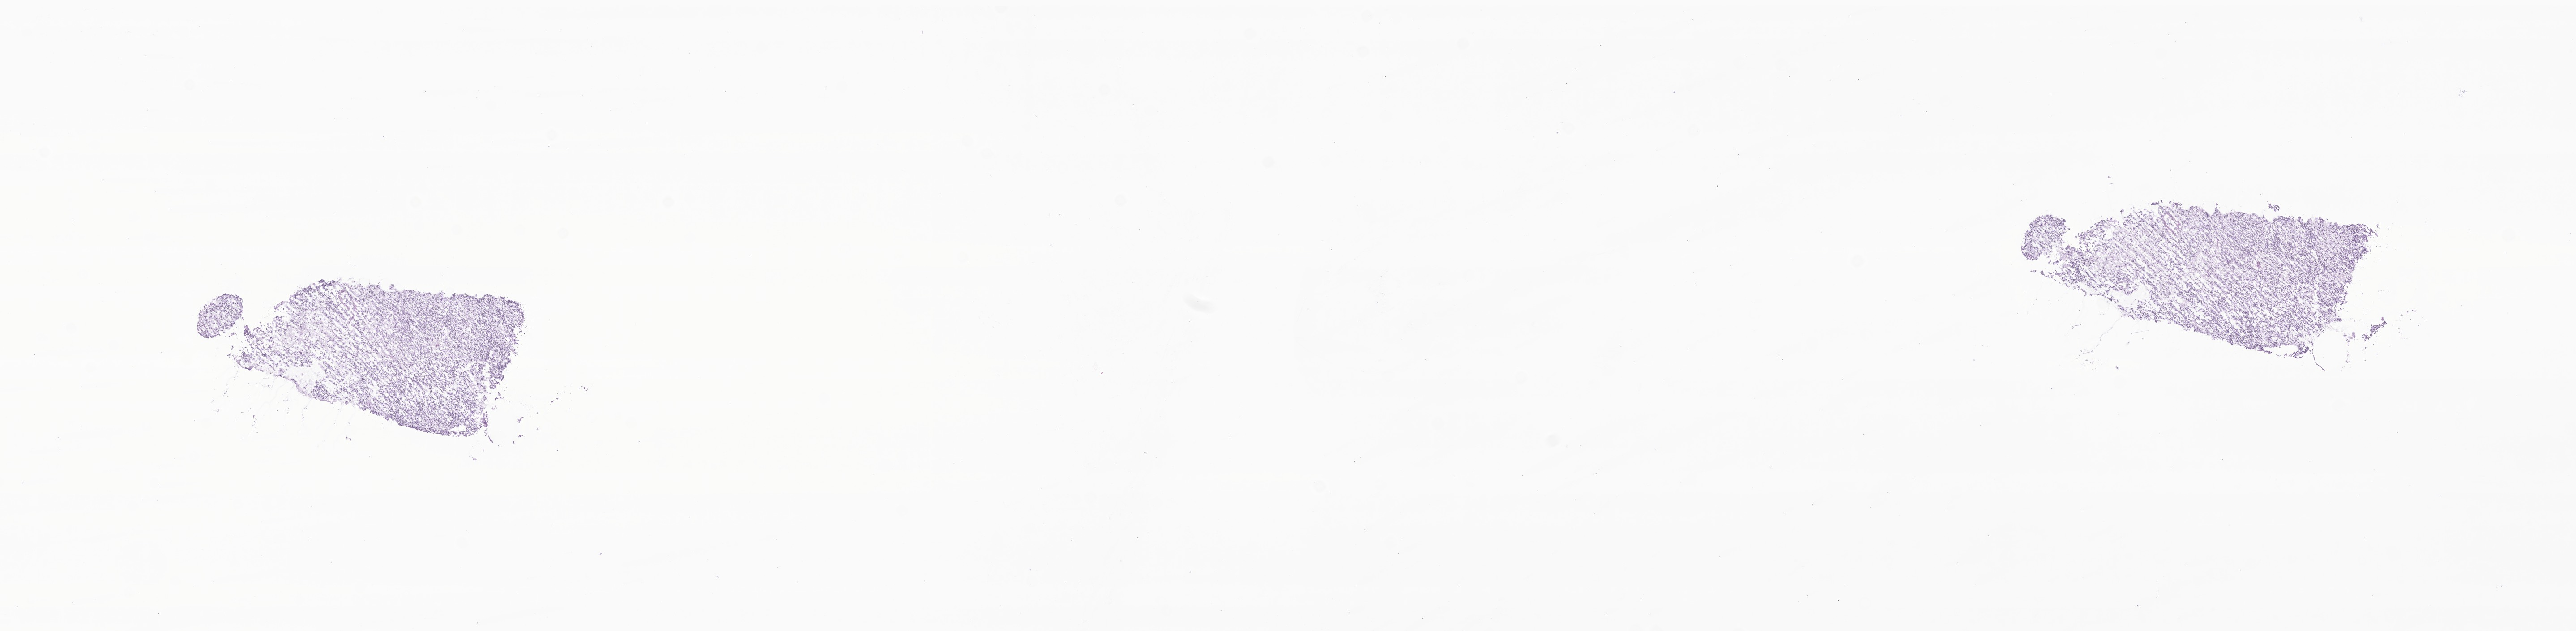
Whole-slide image, H&E stain of tumor tissue from the cerebellum, low-resolution overview of the scanned area, about 24.3 x 5.9 mm, frozen section. Patient male; age 40 months.
* diagnosis: Glioma, malignant